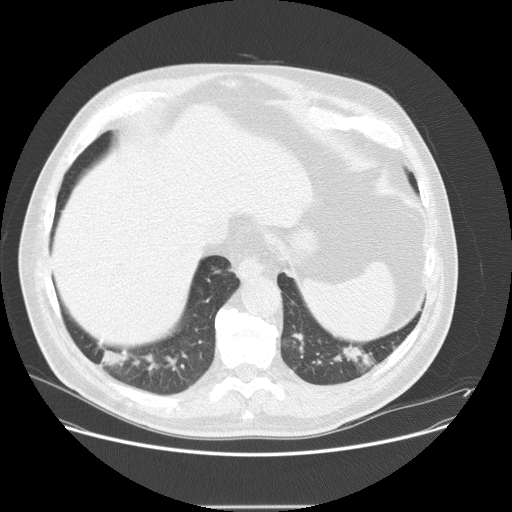
Axial slice from a low-dose chest CT screening exam; baseline annual screen; lung window (W 1500 / L -600 HU); 2.5 mm slice thickness; standard (soft-tissue) reconstruction kernel (STANDARD); 120 kVp; slice 105 of 143 in the series; 512 × 512 image matrix. Male, age 61 years at enrolment.
• Lesion marked by an expert reader, bounding box [x1, y1, x2, y2] px = [90, 336, 144, 386].
• The screening reader recorded 2 non-calcified nodules or masses ≥4 mm on this exam; which of them this box marks is not recorded.
• Lung cancer was diagnosed 41 days after this screen: bronchiolo-alveolar carcinoma, mucinous, right lower lobe, well differentiated (G1), stage IV (AJCC 6th edition), 23 mm at pathology.